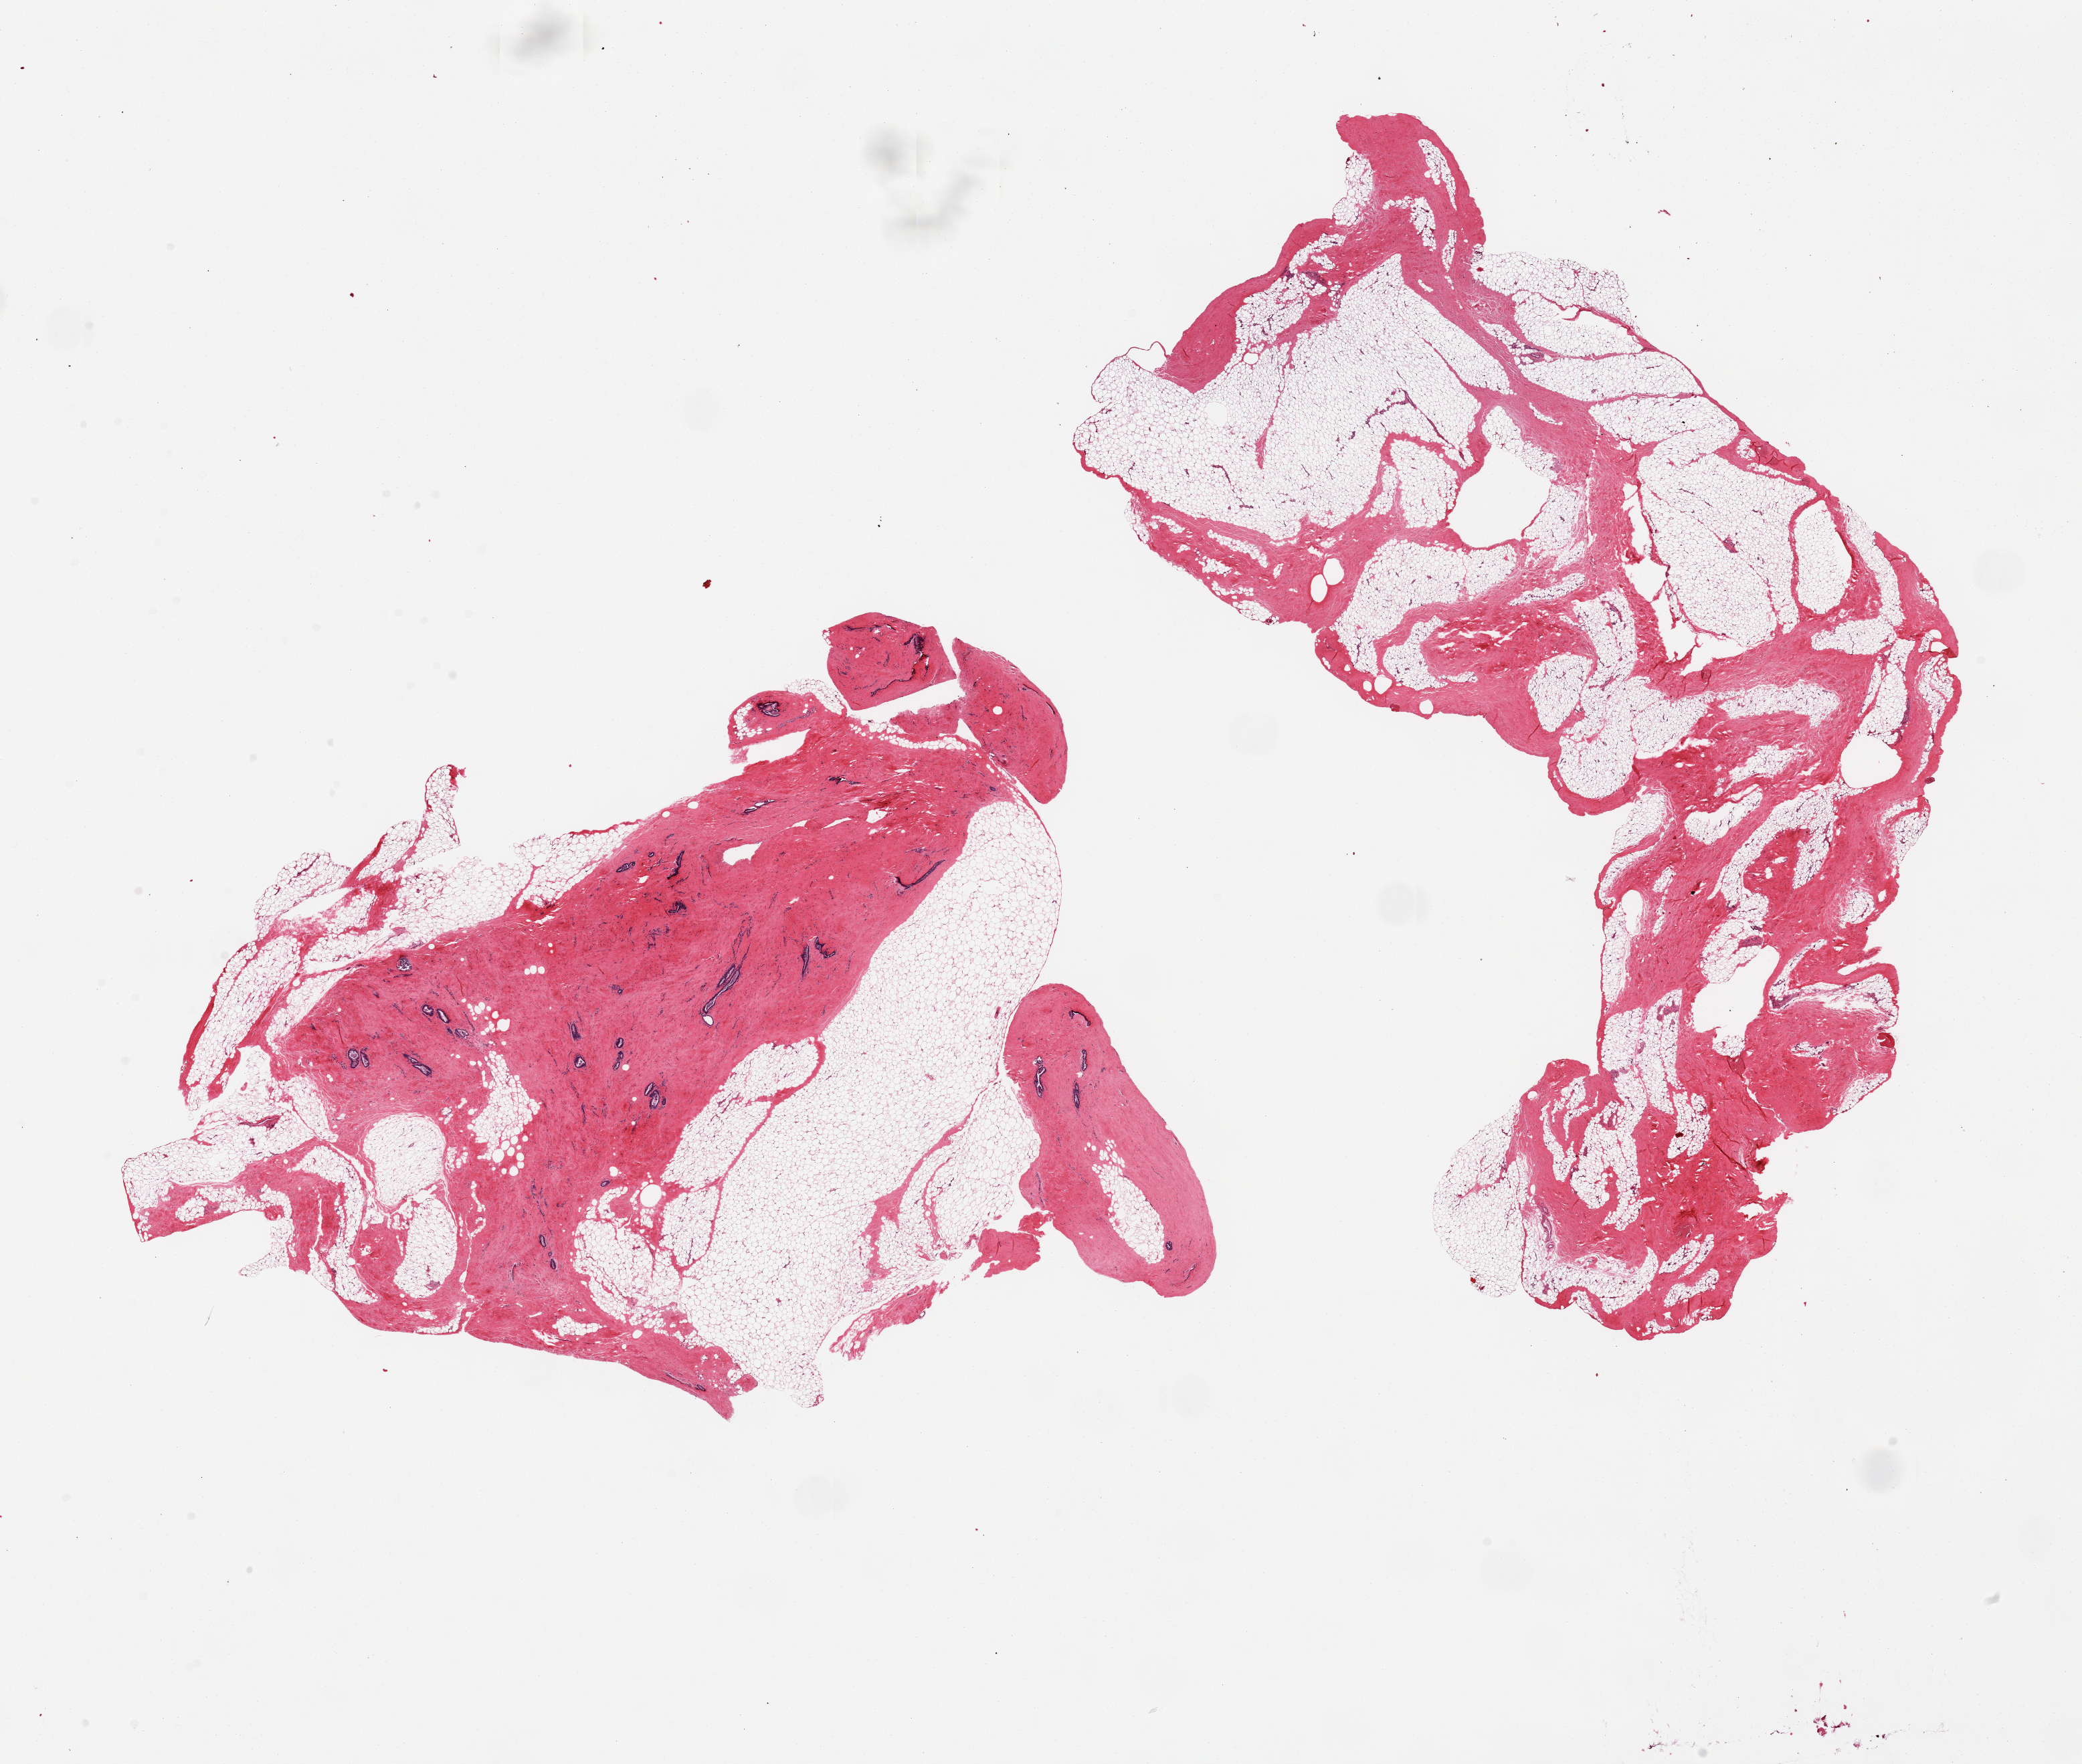
Whole-slide image, hematoxylin and eosin (H&E) stain, brightfield — low-resolution overview of the scanned area, about 24.6 x 20.9 mm, PAXgene-fixed, paraffin-embedded tissue, target tissue: breast, donor tissue sample. Donor: male.
- review note (as recorded): 2 pieces, gynecomastoid stromal/ductal hyperplasia; ductal elements